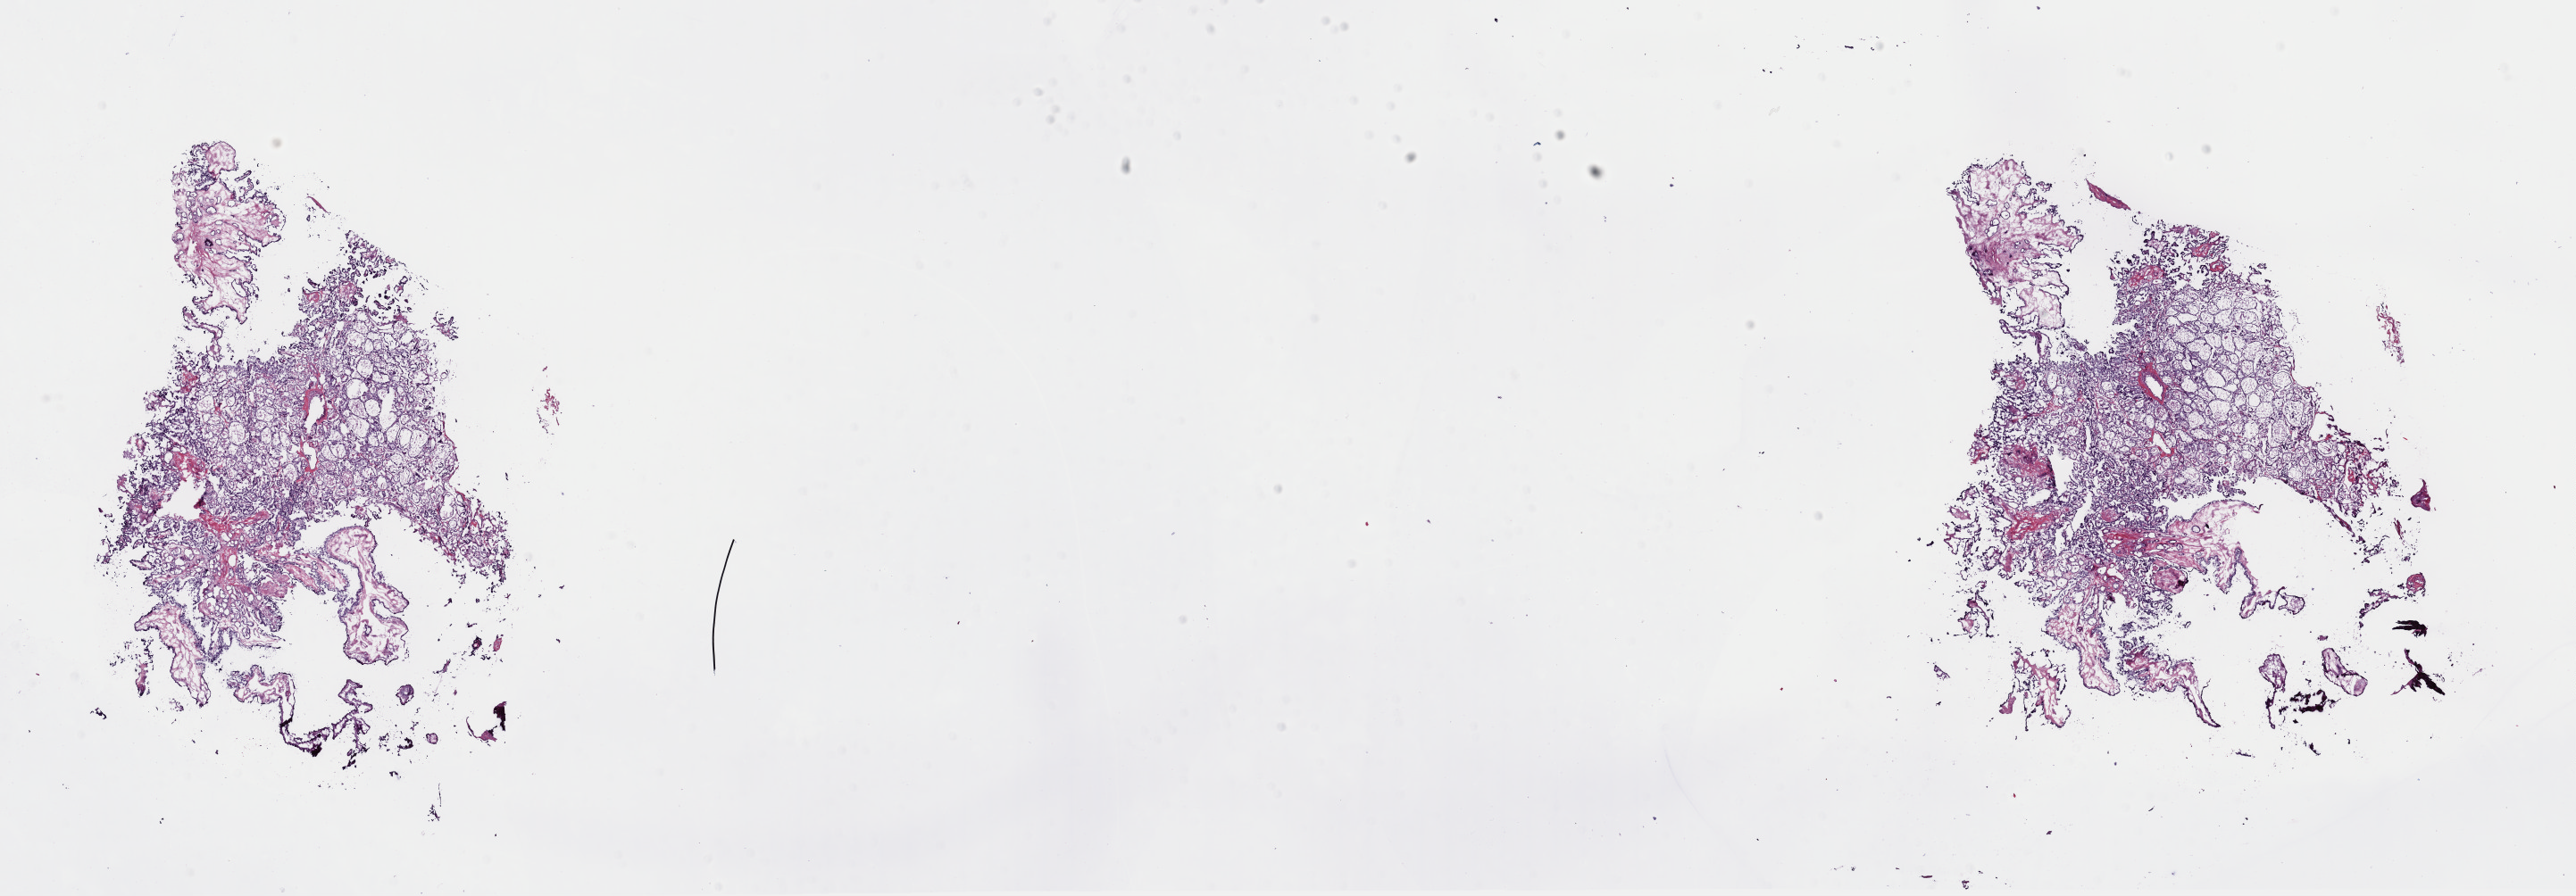
Whole-slide histology image, H&E-stained — a low-resolution overview of the entire scanned area, about 22.8 x 7.9 mm (slide scanned at 40x). Frozen section from the top of the tissue portion. Thyroid, primary tumour sample. Male patient; age at initial diagnosis 50 years. Slide review estimates, as recorded: tumour cells 80%, tumour nuclei 80%, normal cells 0%, stromal cells 20%, necrosis 0%. Infiltration values recorded for this section: lymphocyte infiltration 2%, monocyte infiltration 0%, neutrophil infiltration 0%.
• AJCC pathologic stage: I
• pathologic diagnosis: Papillary adenocarcinoma, NOS
• laterality: left